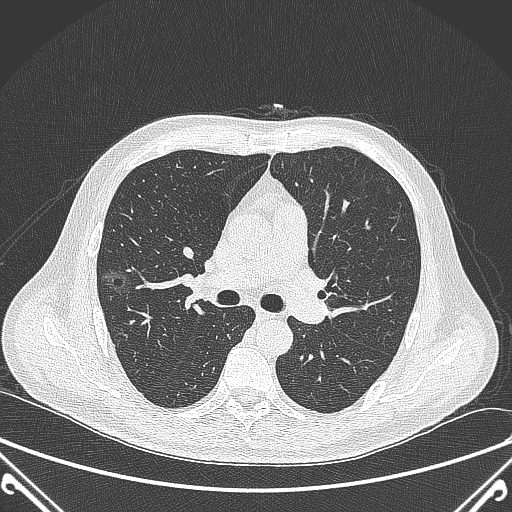
Chest CT, one axial slice; slice 225 of 360 in the series (ordered by position); lung window (W 1500 / L -600 HU); 1 mm slice thickness; 512 × 512 image matrix, field of view 380 × 380 mm. Male patient, age 64 years. Case-level facts recorded for this patient, not image findings: clinical TNM (as recorded): T1c N0 M0.
Annotated regions visible in this slice (rectangle marked by the reading radiologist):
- lung tumour (recorded histology: adenocarcinoma): bounding box (x1, y1, x2, y2) in pixels: (101, 267, 134, 292)